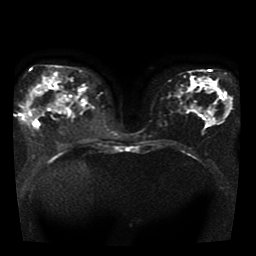
Breast MRI, one axial slice. Position 19 of 41 along the scan axis. Diffusion-weighted series; image 2 of 4 stored at this slice position (different b-values; order by instance number). 1.5 T. 5 mm slice thickness. 256 × 256 image matrix, field of view 330 × 330 mm. Female patient.
Structures marked on this image (manually delineated by an expert):
- tumour on diffusion-weighted imaging: bounding box (x1, y1, x2, y2) in pixels: (26, 115, 39, 122)